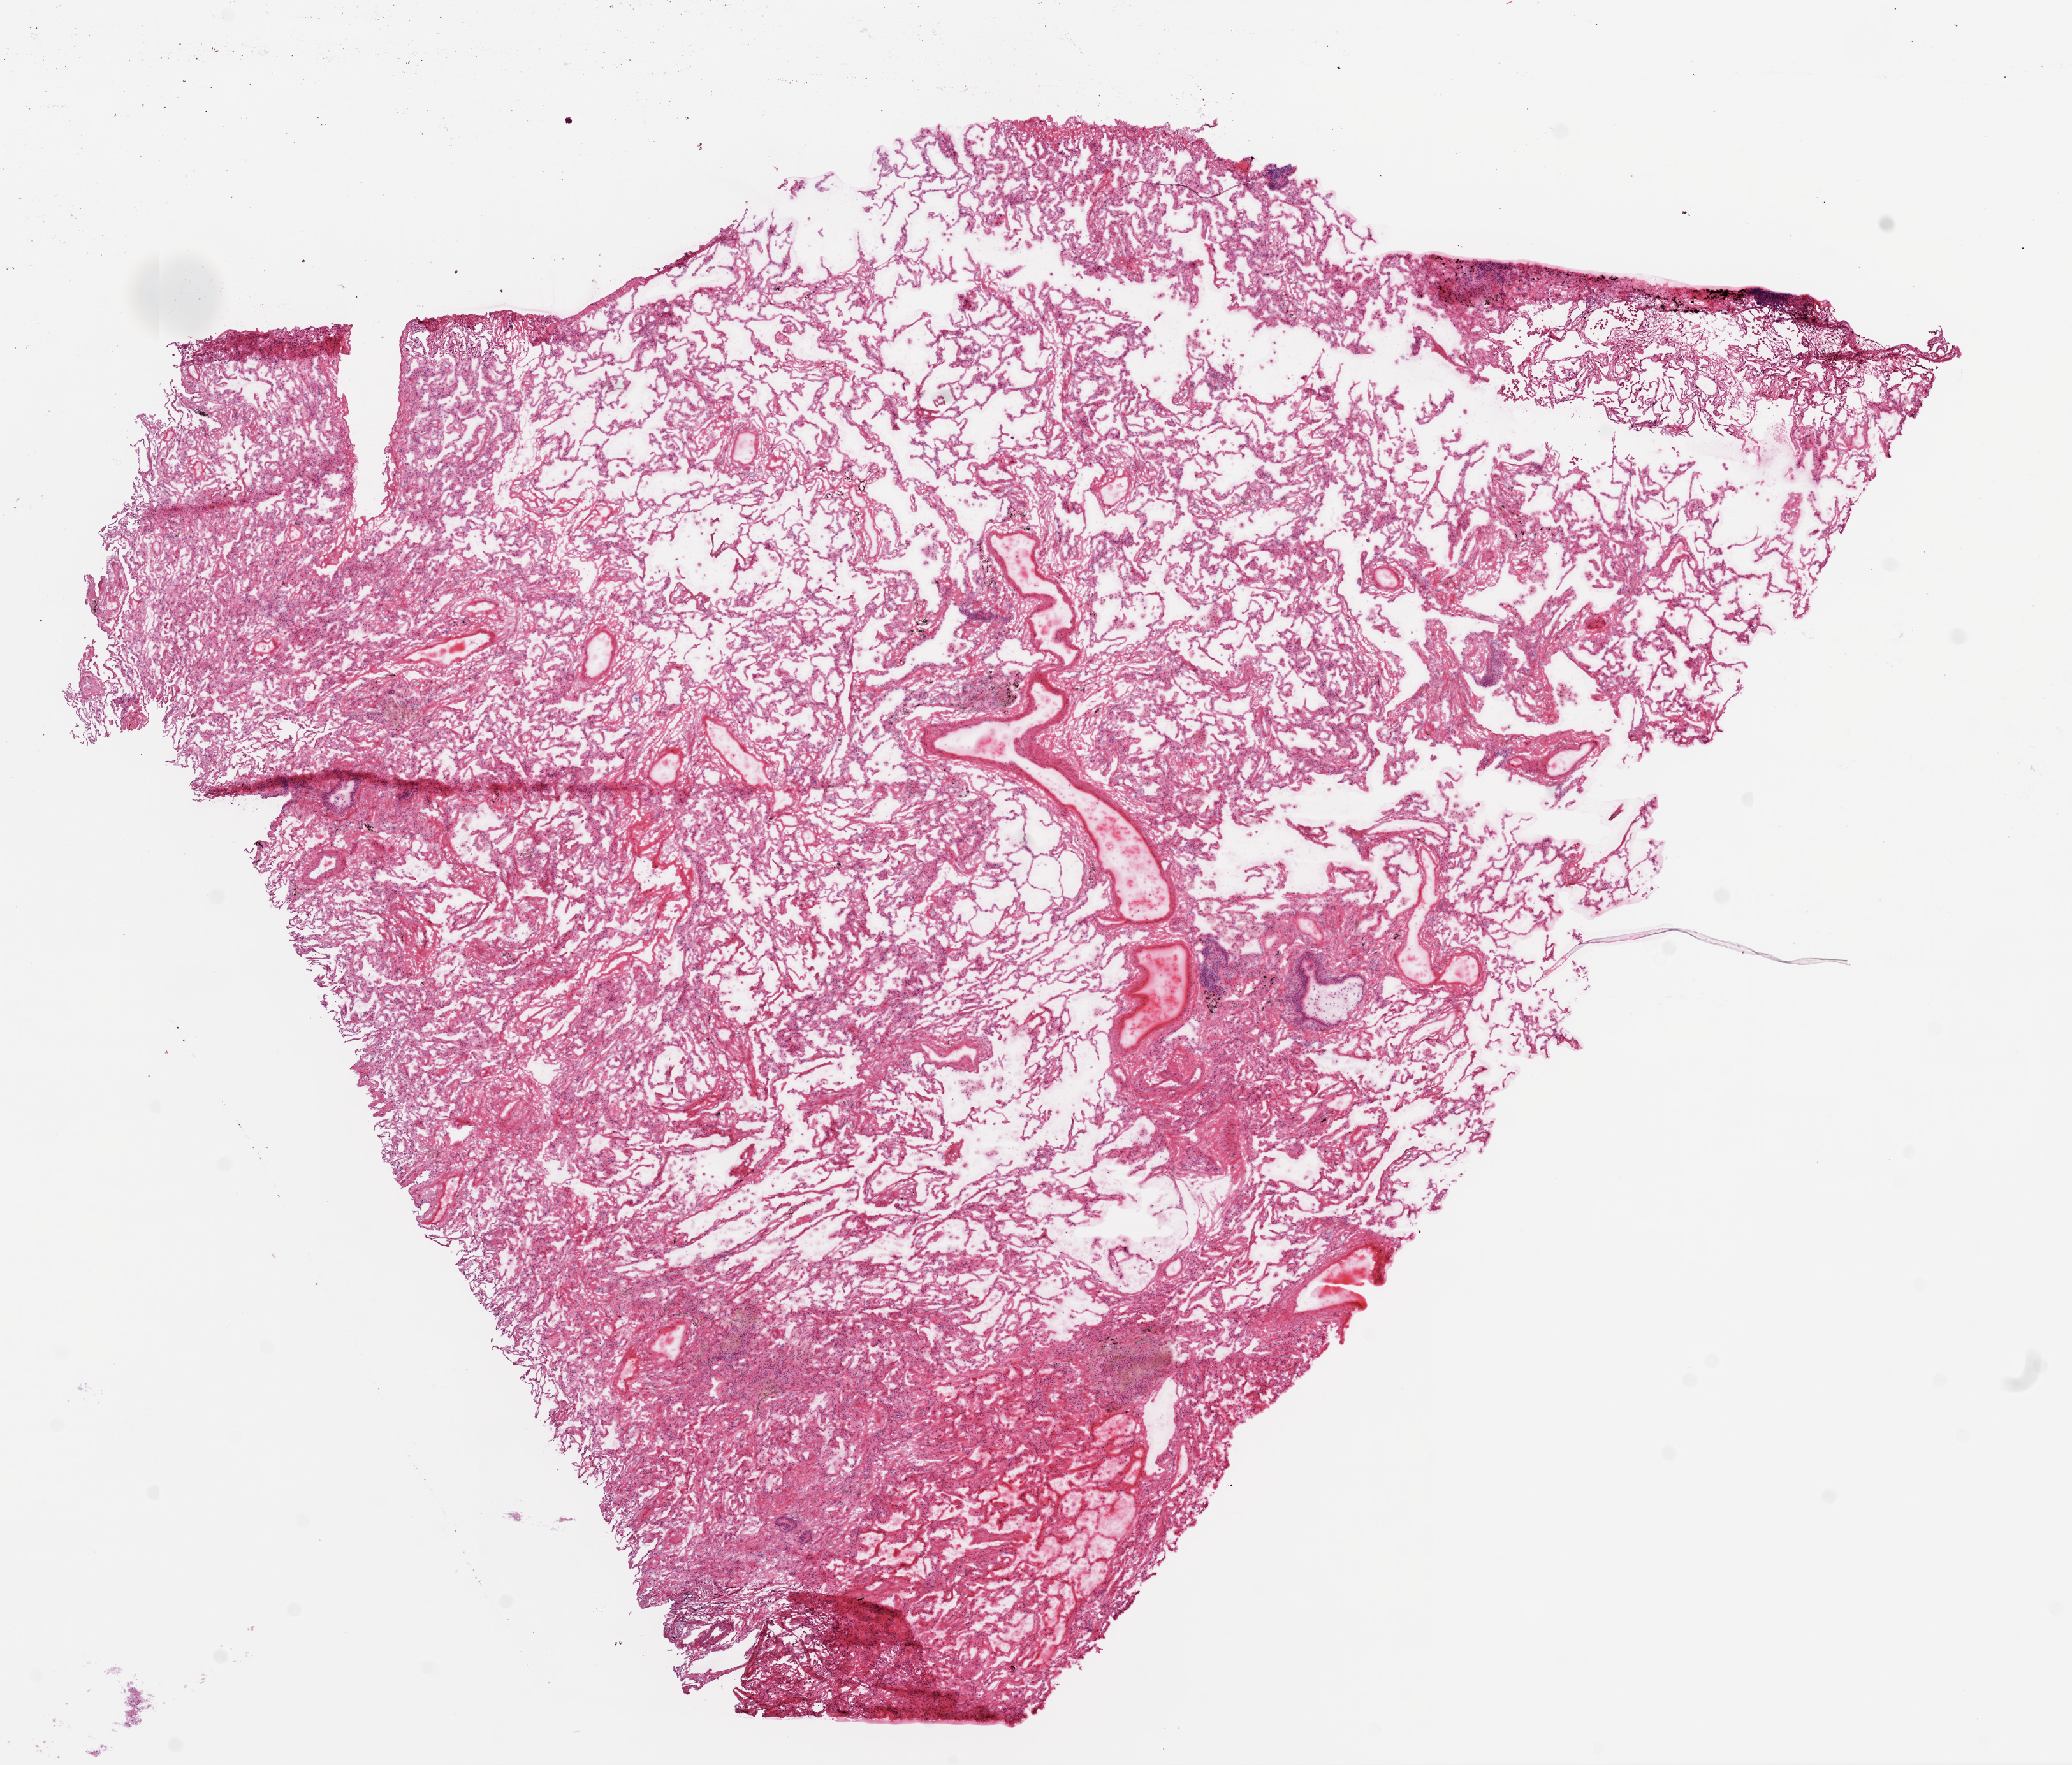
Hematoxylin and eosin (H&E) stained whole-slide image — whole scanned area (about 13.0 x 11.1 mm) shown as a low-resolution overview; frozen section from the top of the tissue portion; solid tissue normal (non-tumour tissue) sample from the lung. Female patient; age at initial diagnosis 73 years.
• this section: solid tissue normal sample (biorepository sample class)
• patient diagnosis: Squamous cell carcinoma, NOS (upper lobe, lung)